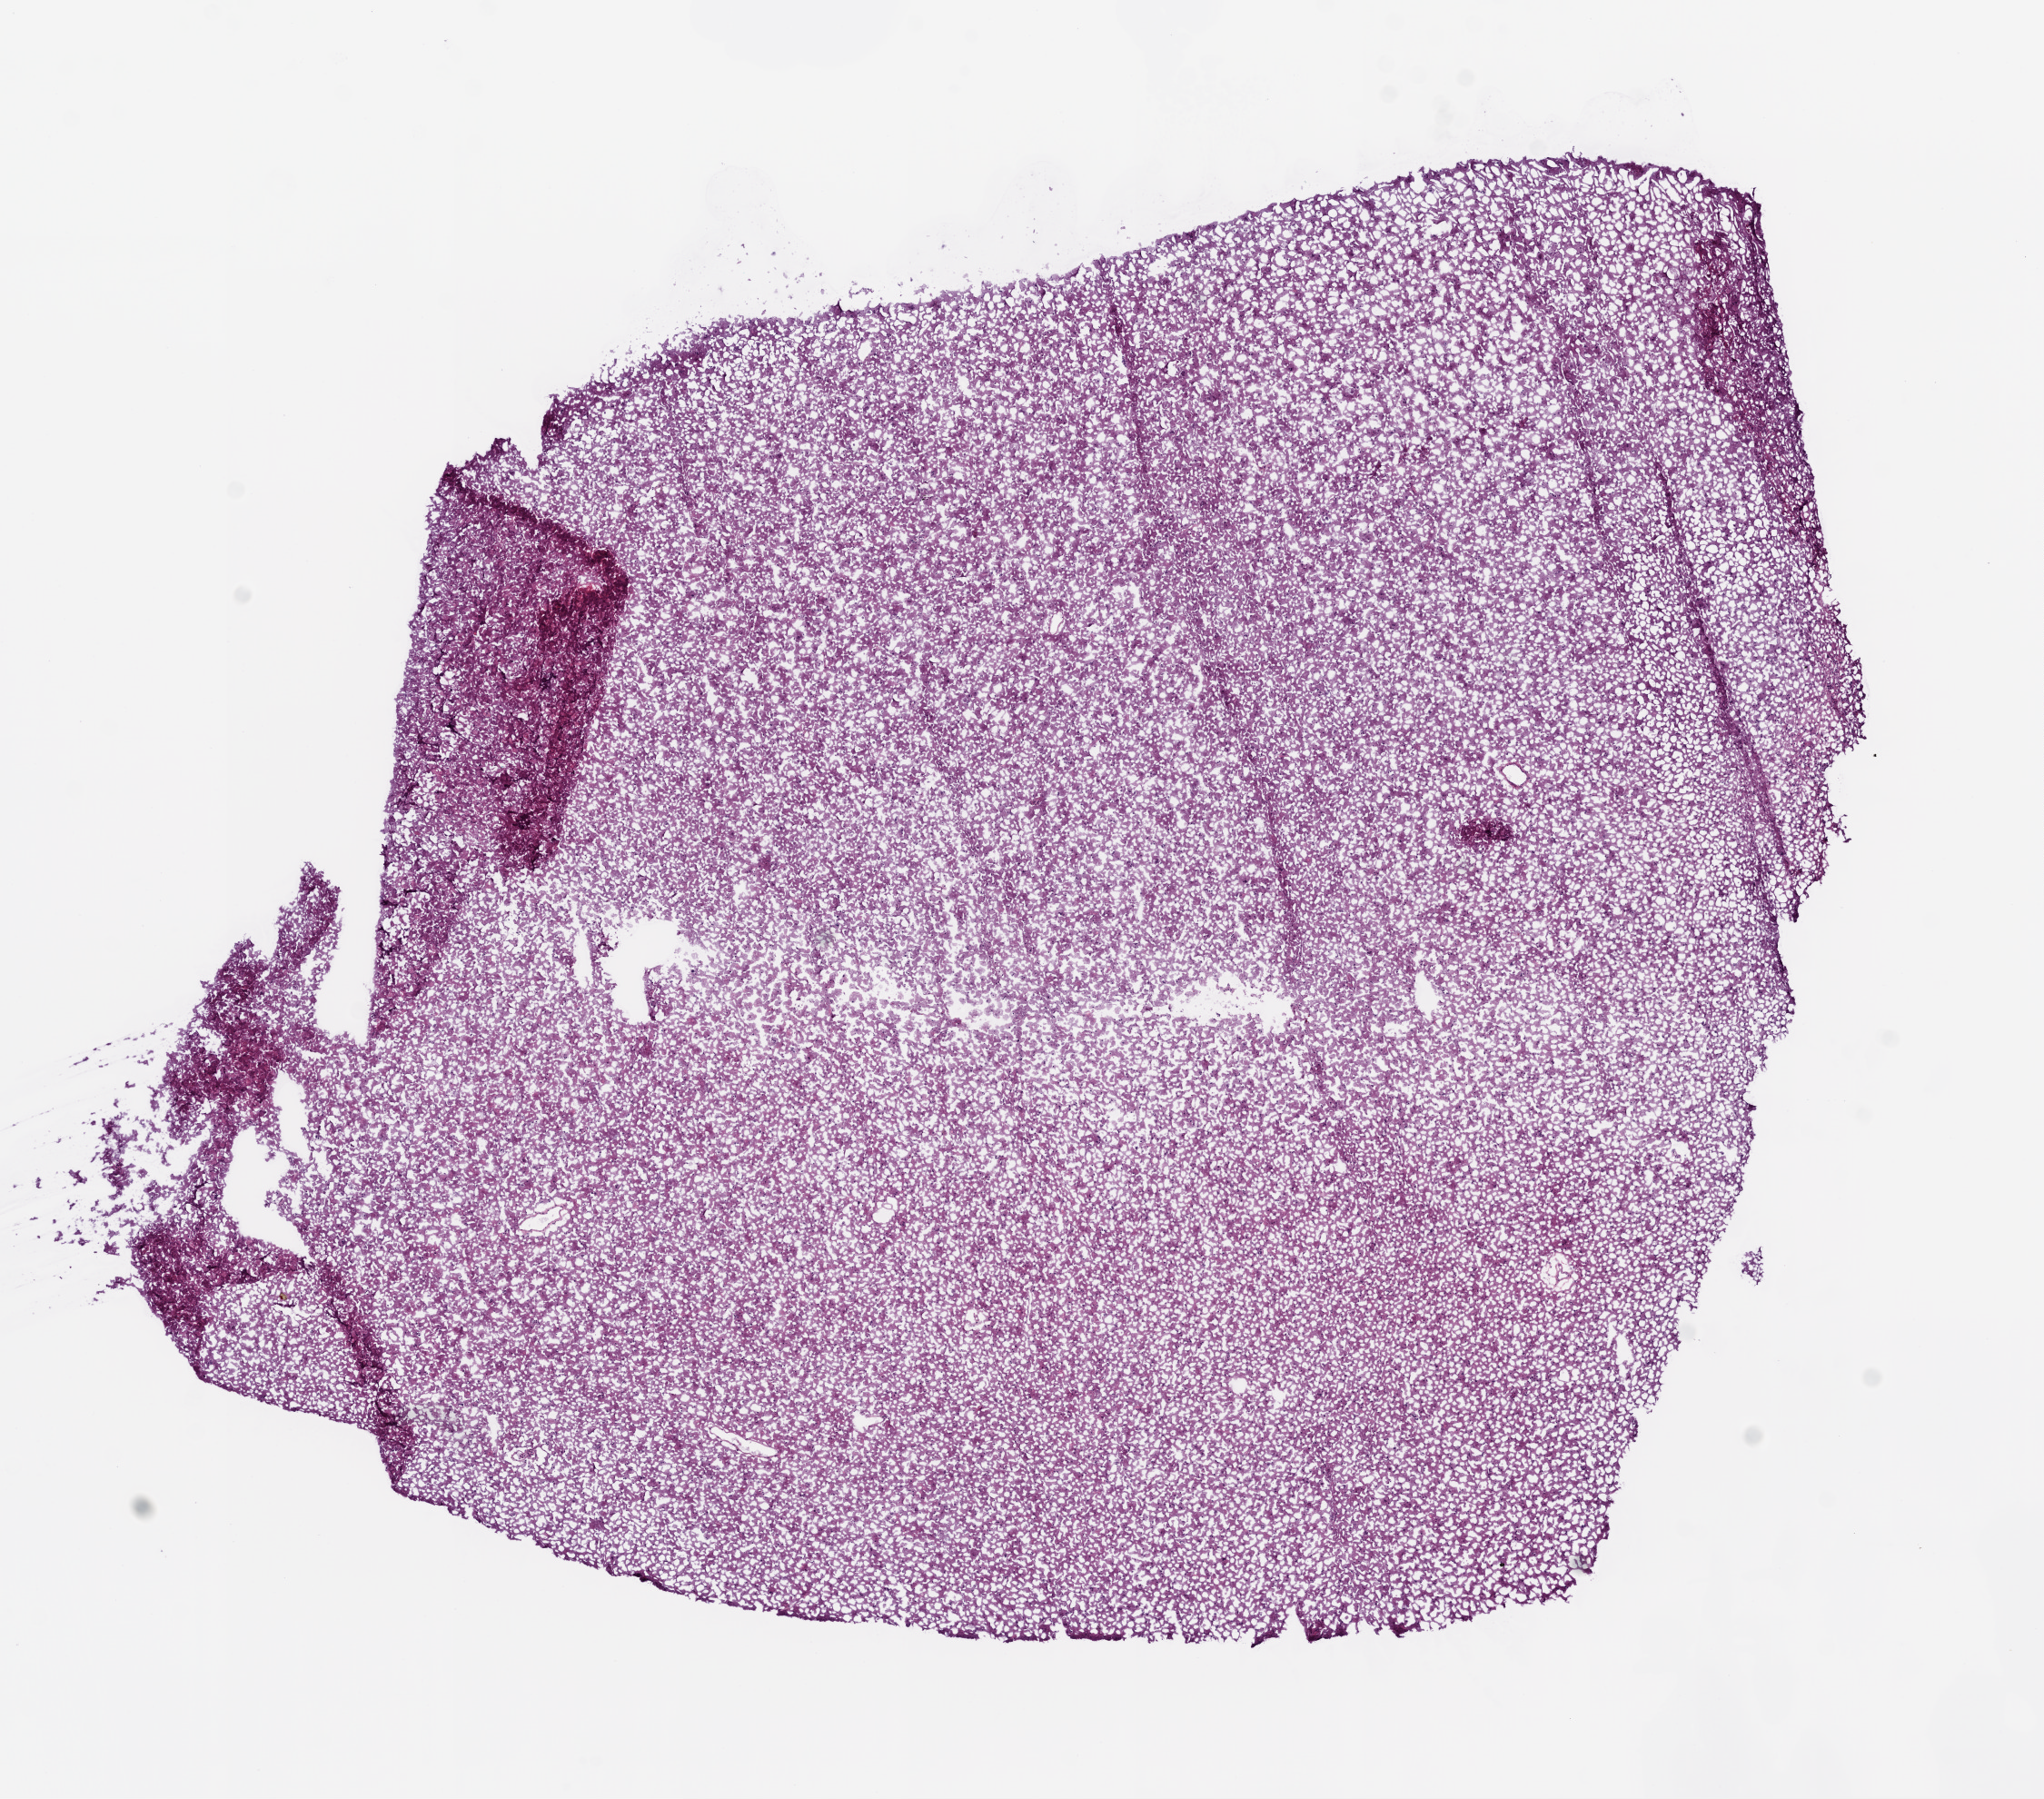
H&E-stained whole-slide image, shown as a low-resolution overview of the whole scanned area (about 9.0 x 7.9 mm, acquisition: 20x scan); frozen section from the bottom of the tissue portion; sample: primary tumour, brain. Female patient; age at initial diagnosis 38 years. Histologic grade: G3 (poorly differentiated). Composition of this section per pathologist review: tumour cells 100%, tumour nuclei 60%, normal cells 0%, stromal cells 0%, necrosis 0%.
Histologic diagnosis: Mixed glioma (cerebrum). Laterality: left.